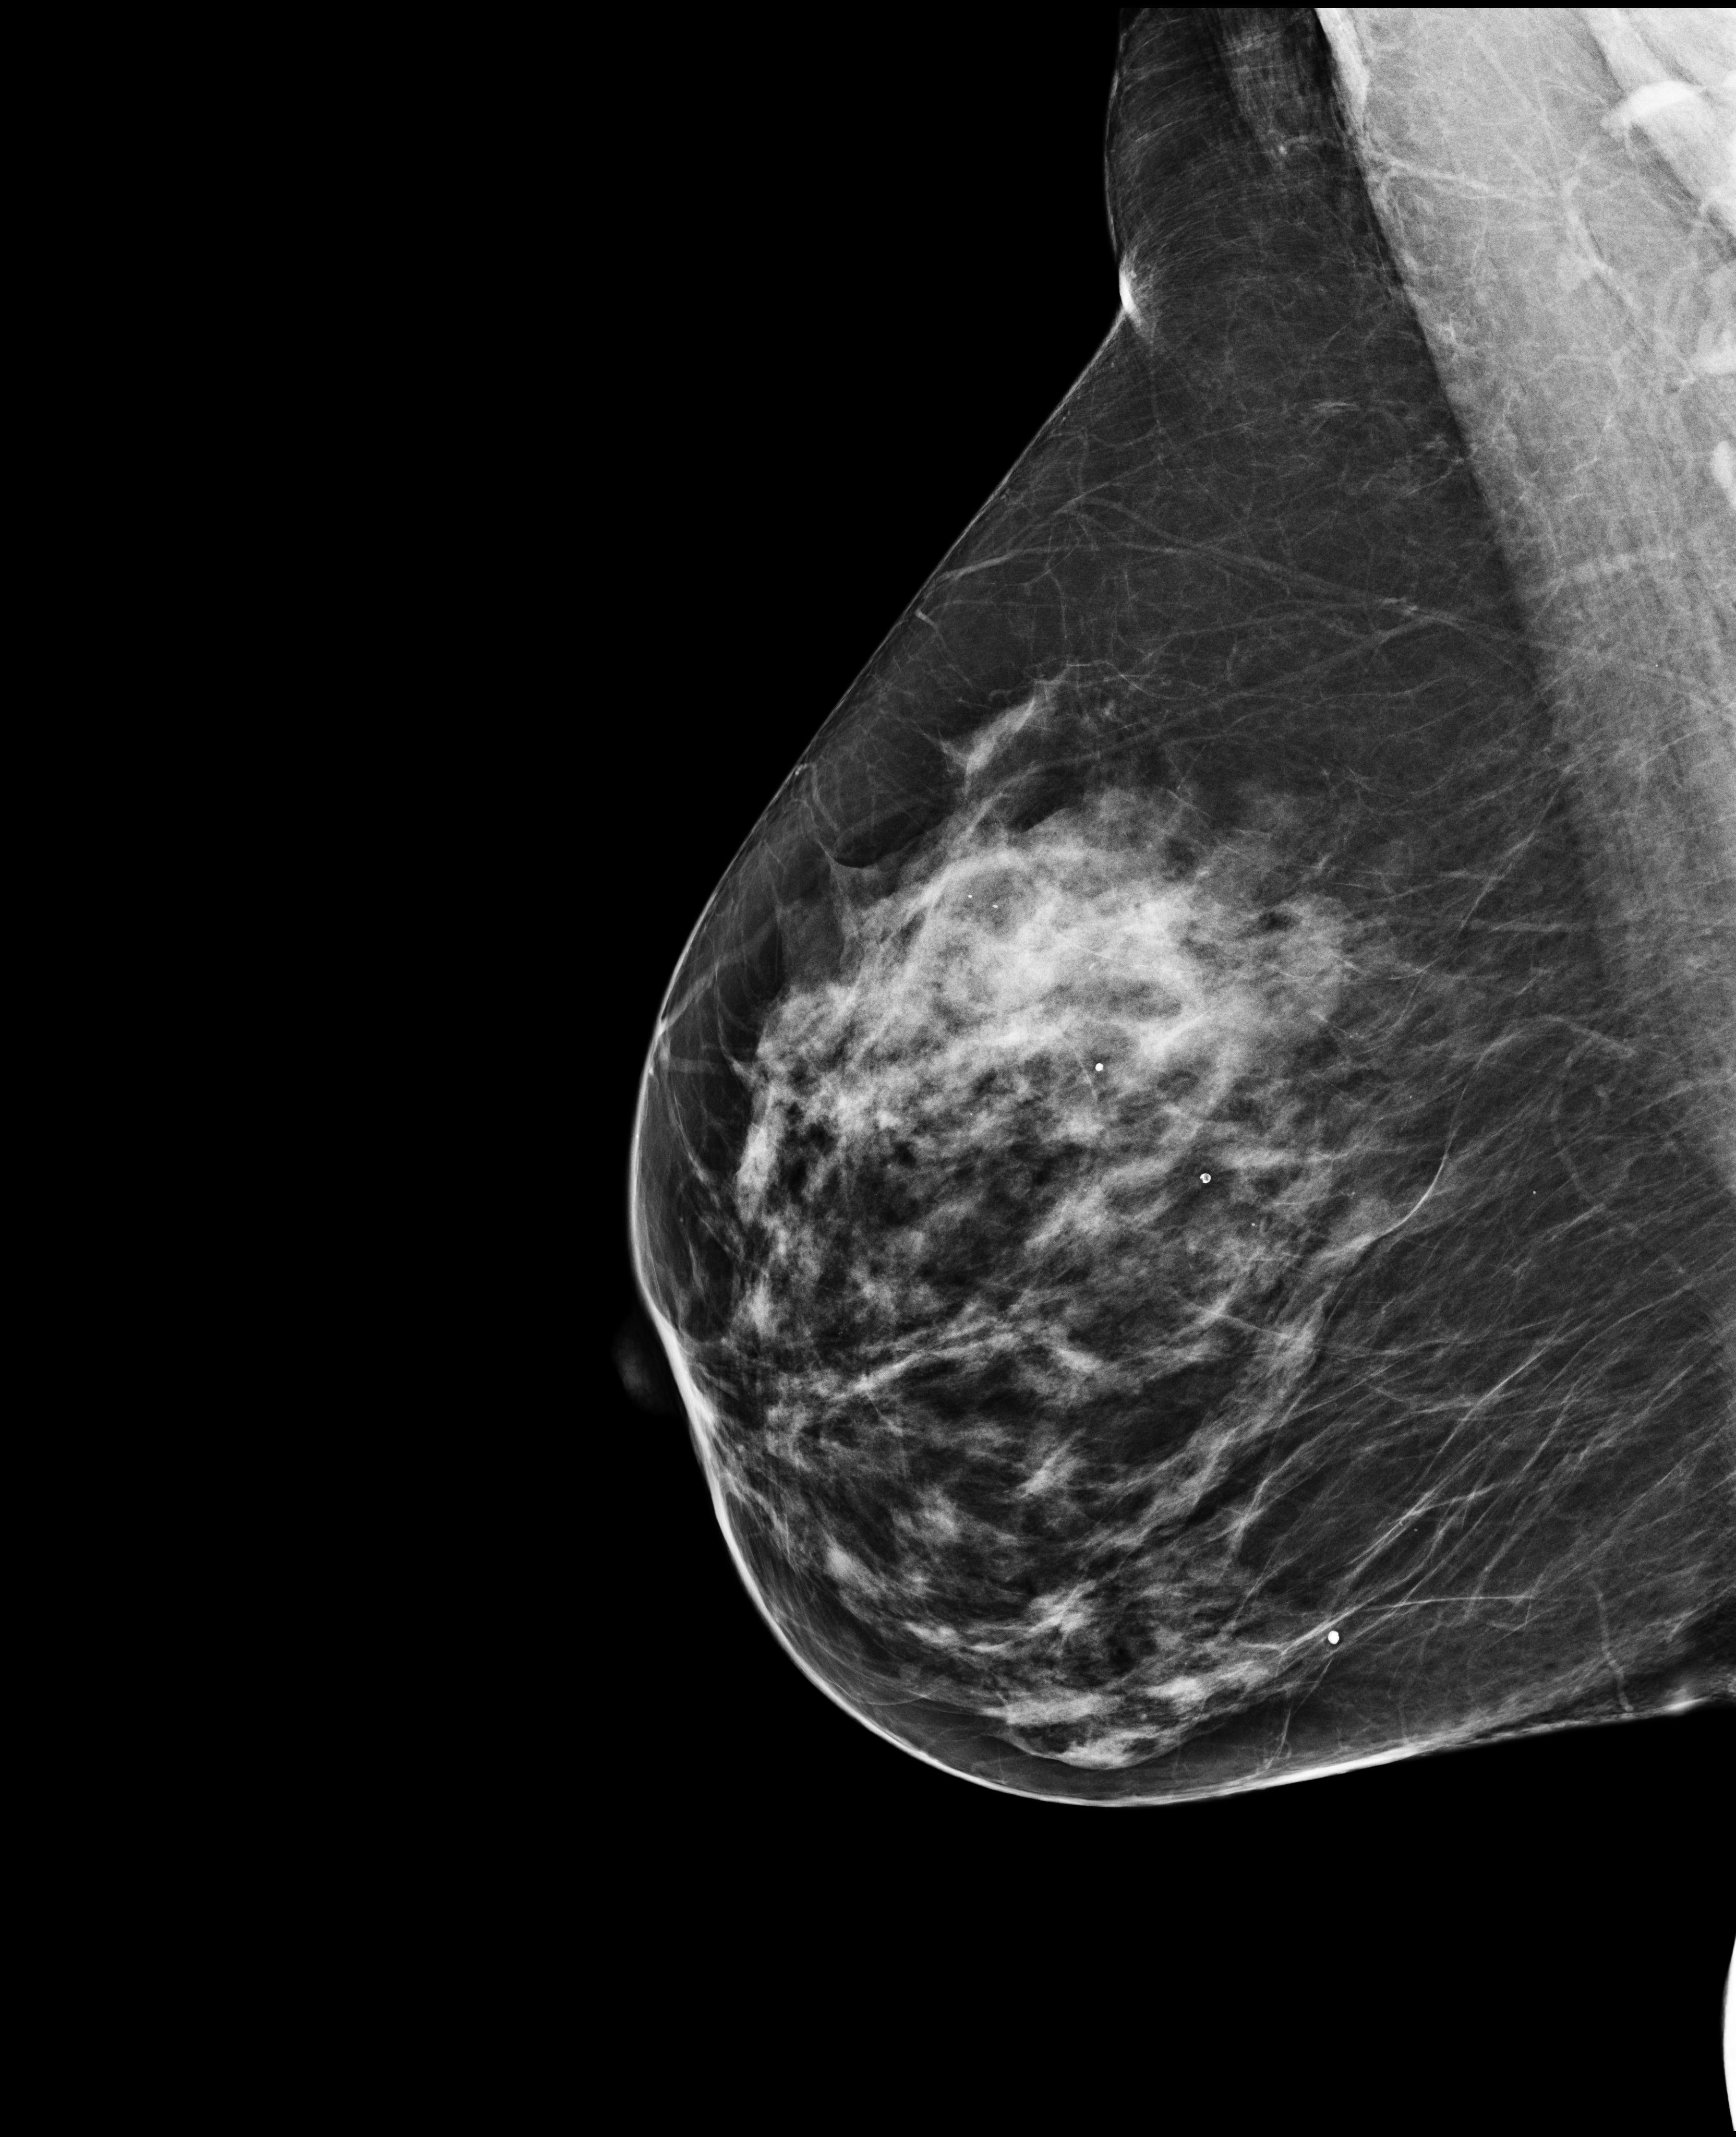
Annual screening mammography examination, compressed breast thickness 62 mm, system: Selenia Dimensions. Female patient, age 63 years.
Image type: full-field digital mammogram. Breast: right. Projection: medio-lateral oblique projection.